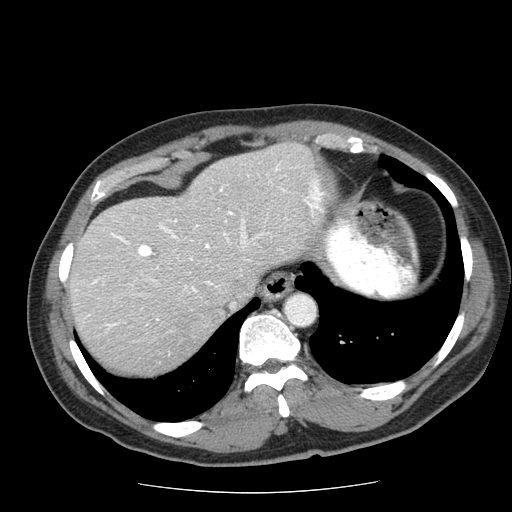
Contrast-enhanced abdominal CT (liver protocol), one axial slice. Slice 52 of 85 in the series (ordered by position). Reconstruction kernel STANDARD. Soft-tissue window (W 400 / L 40 HU). 2.5 mm slice thickness. 512 × 512 image matrix, field of view 360 × 360 mm. From the clinical record (not read from this slice): diagnosis: hepatocellular carcinoma (patient treated with transarterial chemoembolisation; whether this scan precedes or follows treatment is not stated here); TNM stage (as recorded): Stage-IIIA; Child-Pugh class: A; tumour differentiation: well differentiated; tumour nodularity: multinodular.
Annotated regions visible in this slice (semi-automatic segmentation, software-assisted and operator-edited):
- liver parenchyma outside the tumour (the mass and vessels are separate outlines, so this box may not span the whole liver): bounding box <68,142,328,374> (left, top, right, bottom; pixels)
- liver vessels: <88,164,324,328>